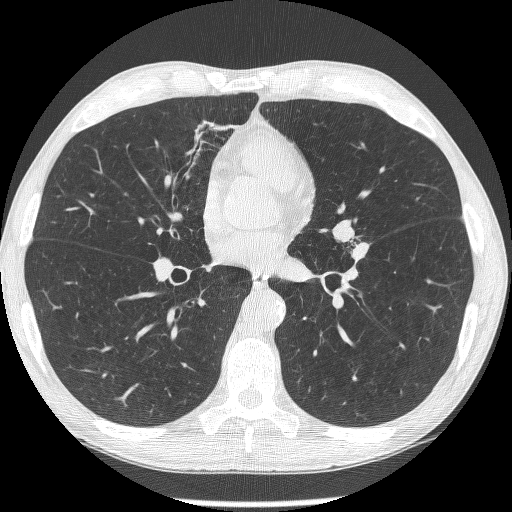
Chest CT (low-dose screening protocol), one axial image, second screening round (one year after baseline), lung window (W 1500 / L -600 HU), 1.25 mm slice thickness, slice 132 of 293 in the series. Male, age 62 years at enrolment. Former smoker at enrolment.
Expert reader's lesion annotation, bounding box <321,217,369,265> (left, top, right, bottom; pixels). The screening reader recorded 2 non-calcified nodules or masses ≥4 mm on this exam; which of them this box marks is not recorded. Later outcome: lung cancer diagnosed 95 days after this screen — small cell carcinoma, NOS, left upper lobe, stage IIIA (AJCC 6th edition).